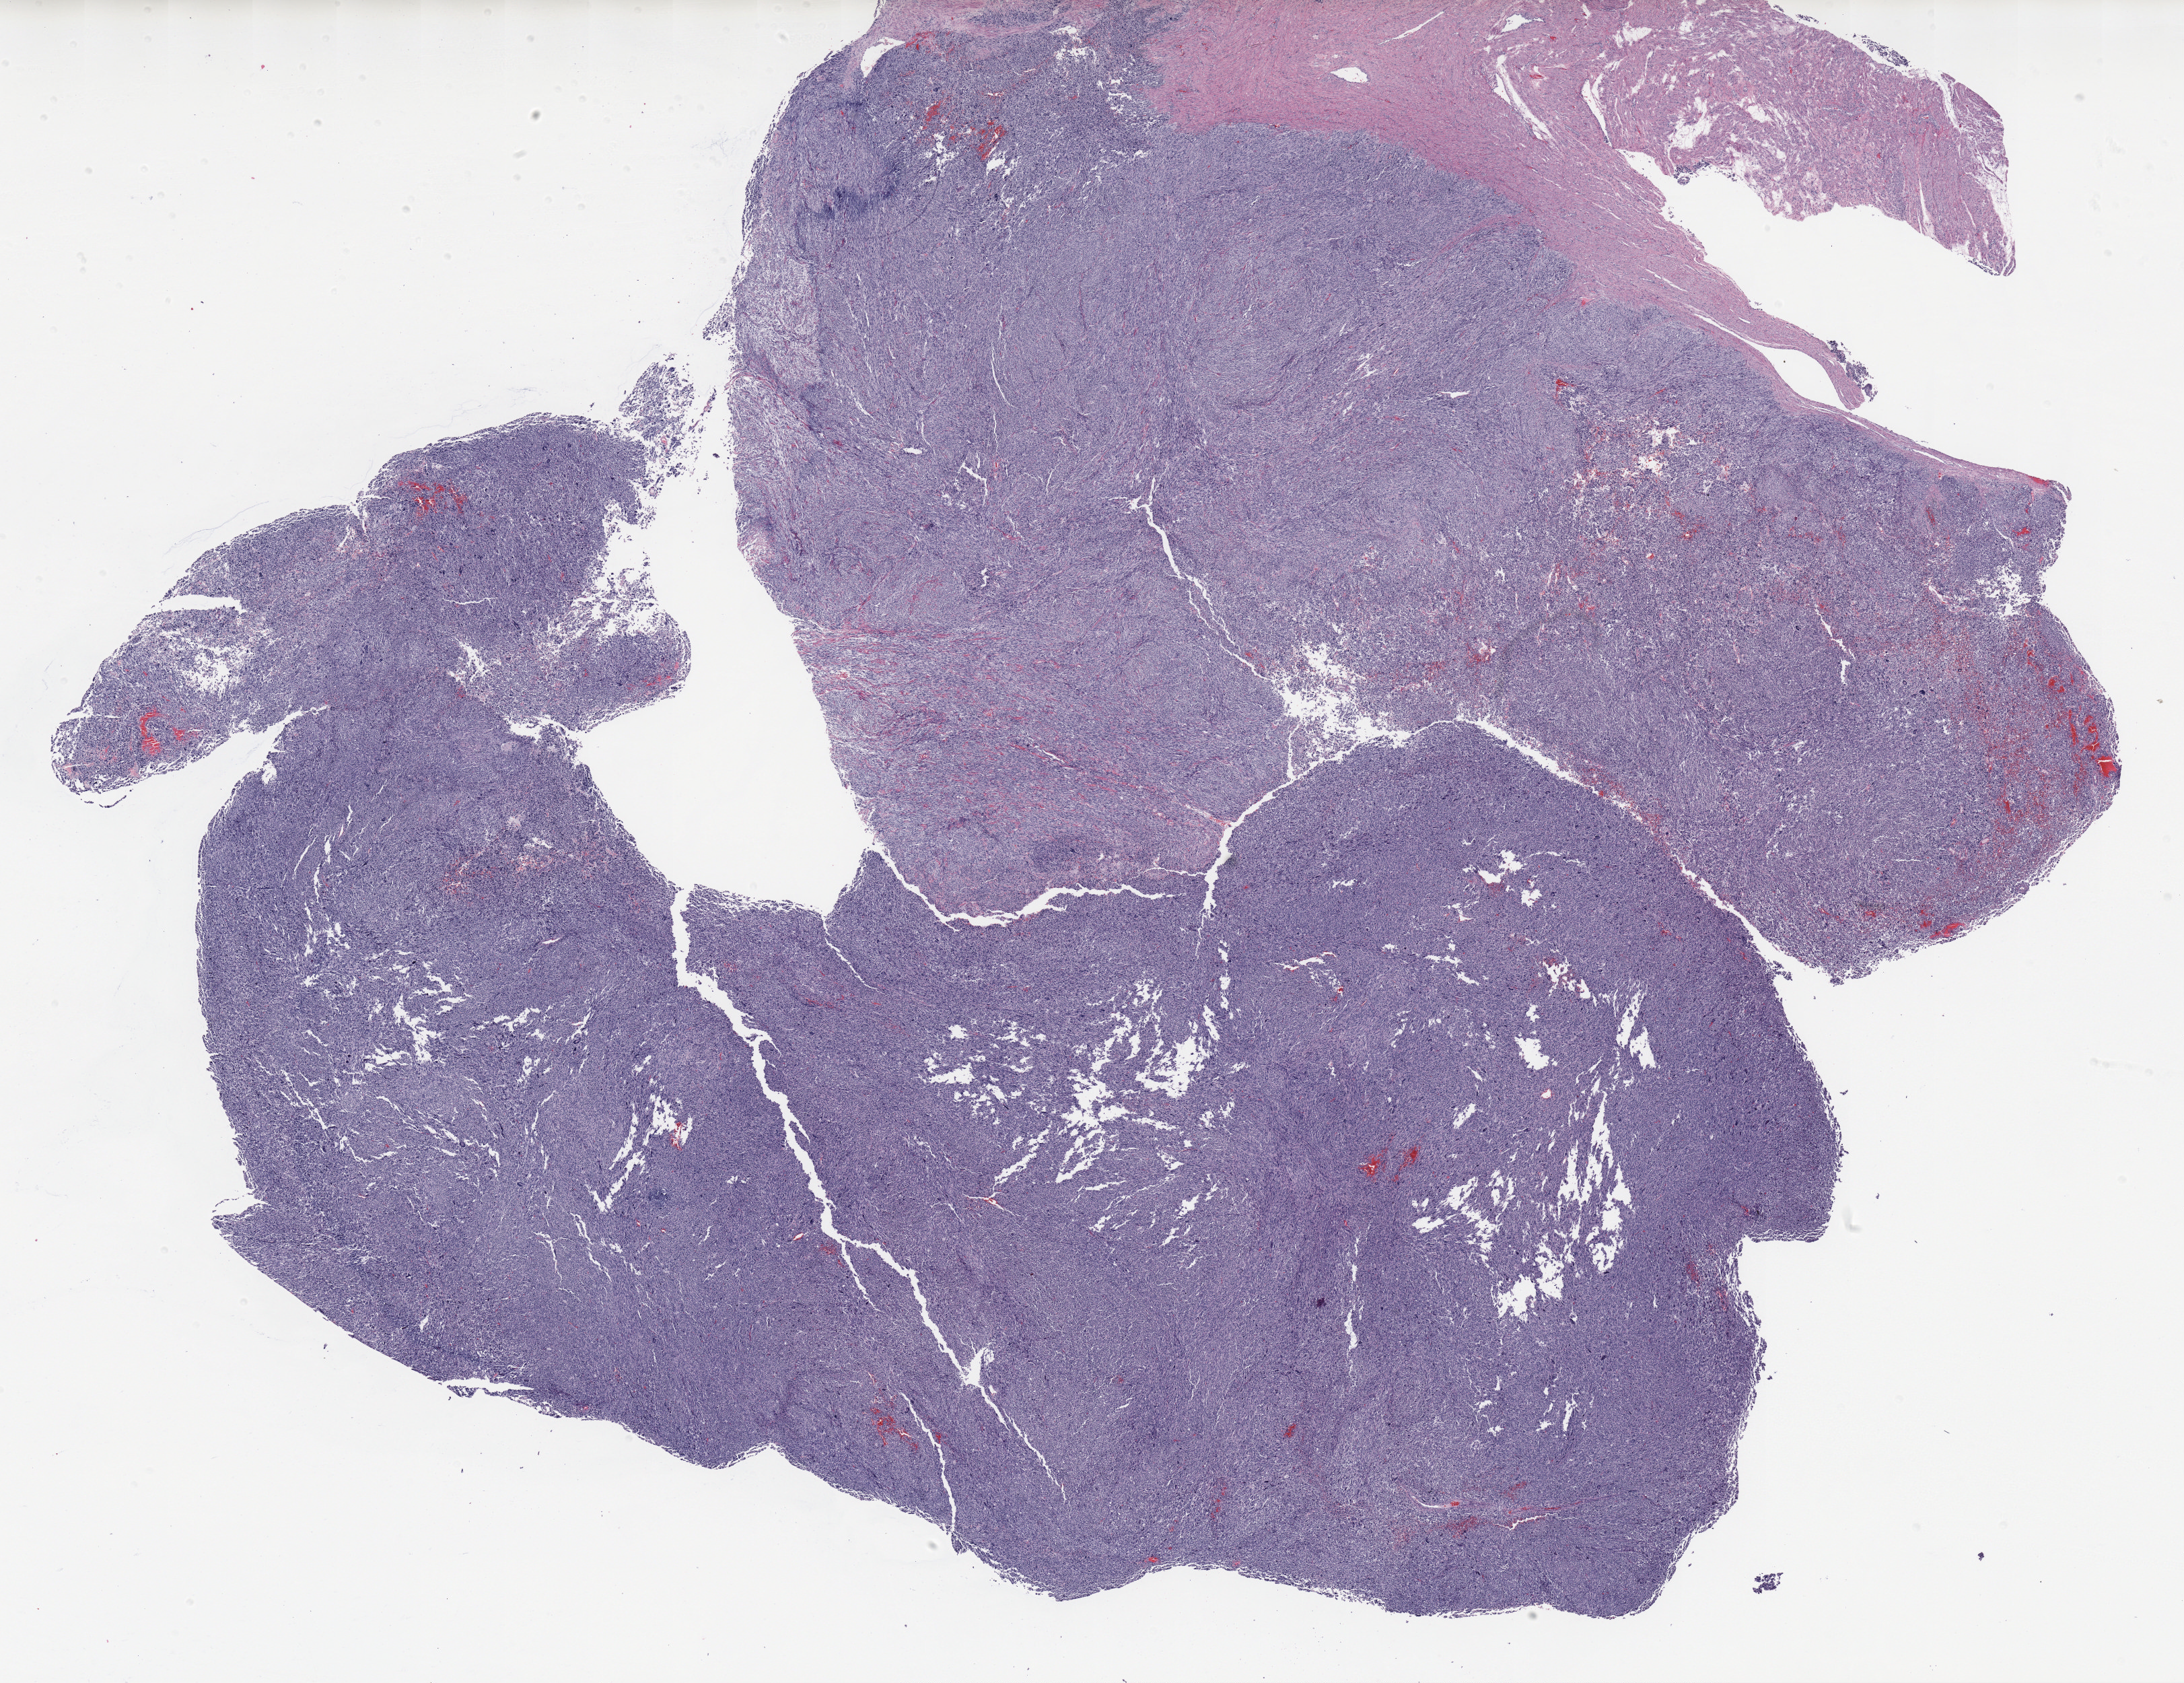
Digitized H&E-stained tissue section (whole slide) — shown as a low-resolution overview of the whole scanned area (about 25.9 x 19.9 mm); formalin-fixed paraffin-embedded (FFPE) diagnostic section; primary tumour sample from the uterus. Patient: female, age at initial diagnosis 63 years.
Histologic diagnosis: Leiomyosarcoma, NOS.